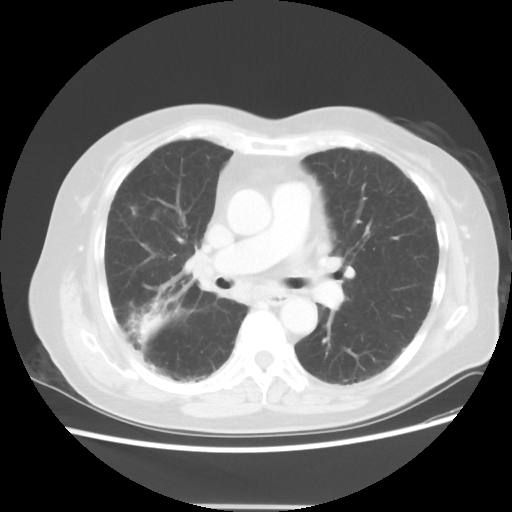
Chest CT, one axial slice. Position 27 of 50 along the scan axis. Reconstruction kernel STANDARD. Lung window (W 1500 / L -600 HU). 5 mm slice thickness. 512 × 512 image matrix, field of view 360 × 360 mm. Patient: female, 72 years. From the clinical record (not read from this slice): clinical TNM (as recorded): T2 N1 M0.
Structures marked on this image (bounding box drawn by a radiologist):
- lung tumour (recorded histology: adenocarcinoma): bounding box [x1, y1, x2, y2] px = [136, 312, 161, 335]